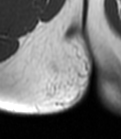
MRI of an extremity soft-tissue mass, one axial slice. Slice 12 of 47 in the series (ordered by position). MR volume resampled by the dataset authors to the PET/CT grid (not the native acquisition matrix). 3.27 mm slice thickness. 121 × 139 image matrix, field of view 118 × 136 mm. Female patient. From the clinical record (not read from this slice): histological type: epithelioid sarcoma; grade: intermediate; site of the primary tumour: right buttock.
Structures marked on this image (expert contour drawn on MRI and transferred to this co-registered scan by the dataset authors):
- gross tumour volume including surrounding oedema: bounding box [x1, y1, x2, y2] px = [45, 55, 83, 101]